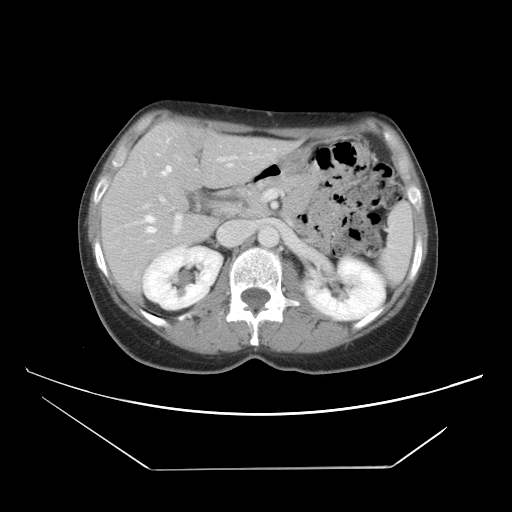
Contrast-enhanced abdominal CT, one axial slice. Position 25 of 42 along the scan axis. 120 kVp. Intravenous contrast given. Soft-tissue window (W 400 / L 40 HU). 5 mm slice thickness. 512 × 512 image matrix, field of view 399 × 399 mm. Female patient, age 52 years. From the clinical record (not read from this slice): diagnosis: colorectal cancer liver metastases, imaged before liver resection; multiple liver metastases: yes; largest metastasis: 5.5 cm.
Structures marked on this image (expert manual segmentation):
- hepatic veins: box from (x=135, y=137) to (x=233, y=234) px
- liver: (x=103, y=122)–(x=291, y=291)
- planned liver remnant (the part of the liver to remain after resection): (x=113, y=122)–(x=219, y=201)
- portal vein (with intrahepatic branches): (x=144, y=155)–(x=270, y=233)